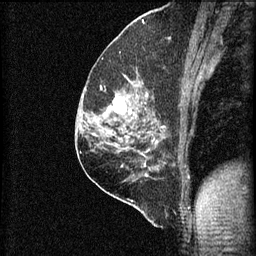
Breast MRI (dynamic contrast-enhanced), one sagittal slice. Slice 38 of 60 in the series (ordered by position). 3 images stored at this slice position (order not interpretable as contrast timing). 1.5 T. TE 4.2 ms, TR 8.2 ms. 2 mm slice thickness. 256 × 256 image matrix. Patient: female, 59 years.
Structures marked on this image (semi-automatically segmented with operator editing):
- analysis volume of interest (the breast-tissue region the enhancement analysis was run in; not a lesion): bounding box (x1, y1, x2, y2) in pixels: (92, 74, 155, 131)
- tumour enhancement mask (voxels above the 70 % enhancement threshold inside the analysis volume of interest): (108, 94, 149, 115)